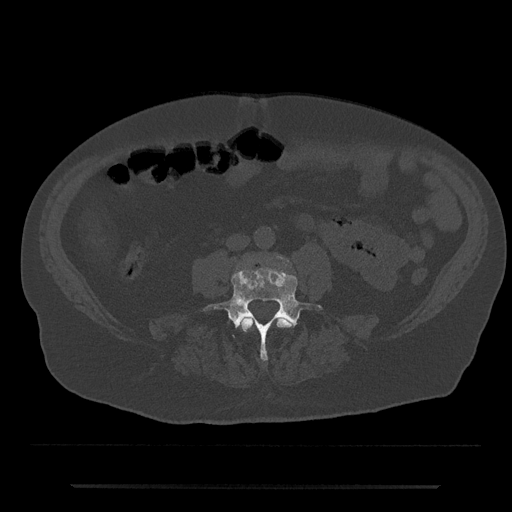
CT including the spine, one axial slice. Slice 363 of 797 in the series (ordered by position). Reconstruction kernel Br40s/3. Bone window (W 1800 / L 400 HU). 0.5 mm slice thickness. 512 × 512 image matrix, field of view 434 × 434 mm. Patient: male, 80 years. From the clinical record (not read from this slice): primary cancer: prostate.
Structures marked on this image (semi-automatic segmentation, software-assisted and operator-edited):
- L3 vertebra: bounding box (x1, y1, x2, y2) in pixels: (239, 317, 293, 332)
- L4 vertebra: (204, 268, 322, 361)